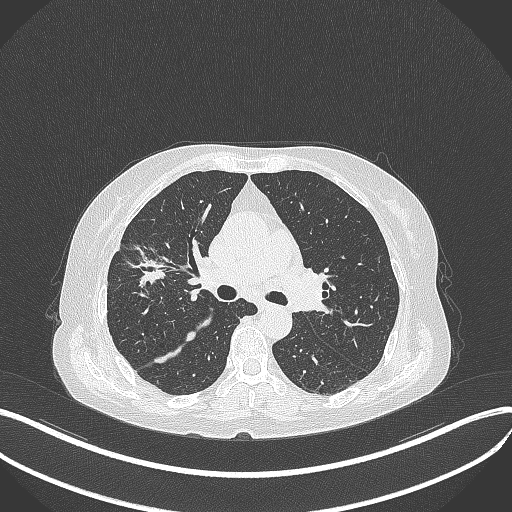
Chest CT, one axial slice. Slice 244 of 429 in the series (ordered by position). 120 kVp. Lung window (W 1500 / L -600 HU). 1 mm slice thickness. 512 × 512 image matrix, field of view 400 × 400 mm. Female patient, age 69 years. Case-level facts recorded for this patient, not image findings: clinical TNM (as recorded): T1b N3 M0.
Annotated regions visible in this slice (bounding box drawn by a radiologist):
- lung tumour (recorded histology: small cell carcinoma): box from (x=116, y=246) to (x=173, y=292) px